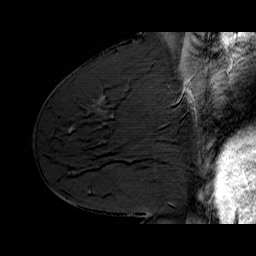
Breast MRI (dynamic contrast-enhanced), one sagittal slice. Position 30 of 60 along the scan axis. Dynamic contrast-enhanced series, time point 2 of 6 at this slice position (early post-contrast). 1.5 T. TE 6.4 ms, TR 32.9 ms. 256 × 256 image matrix. Female patient. Case-level facts recorded for this patient, not image findings: setting: breast cancer imaged before/during neoadjuvant chemotherapy; receptor status: HER2-positive.
Outlined on this slice (semi-automatically segmented with operator editing):
- analysis volume of interest (the breast-tissue region the enhancement analysis was run in; not a lesion): bounding box [x1, y1, x2, y2] px = [143, 62, 210, 124]
- tumour enhancement mask (voxels above the 100 % enhancement threshold inside the analysis volume of interest): [183, 76, 194, 101]